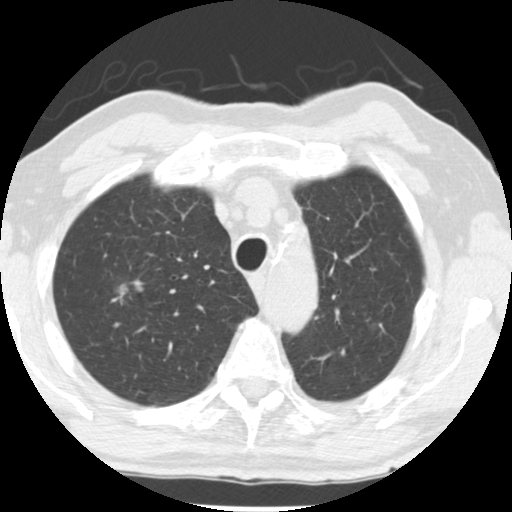
Low-dose screening chest CT, one axial slice; position 199 of 252 along the scan axis; reconstruction kernel STANDARD; lung window (W 1500 / L -600 HU); 512 × 512 image matrix, field of view 313 × 313 mm.
Annotated regions visible in this slice (expert manual segmentation):
- lesion 1 (tumor, upper lobe of right lung): bounding box [x1, y1, x2, y2] px = [112, 285, 128, 304]